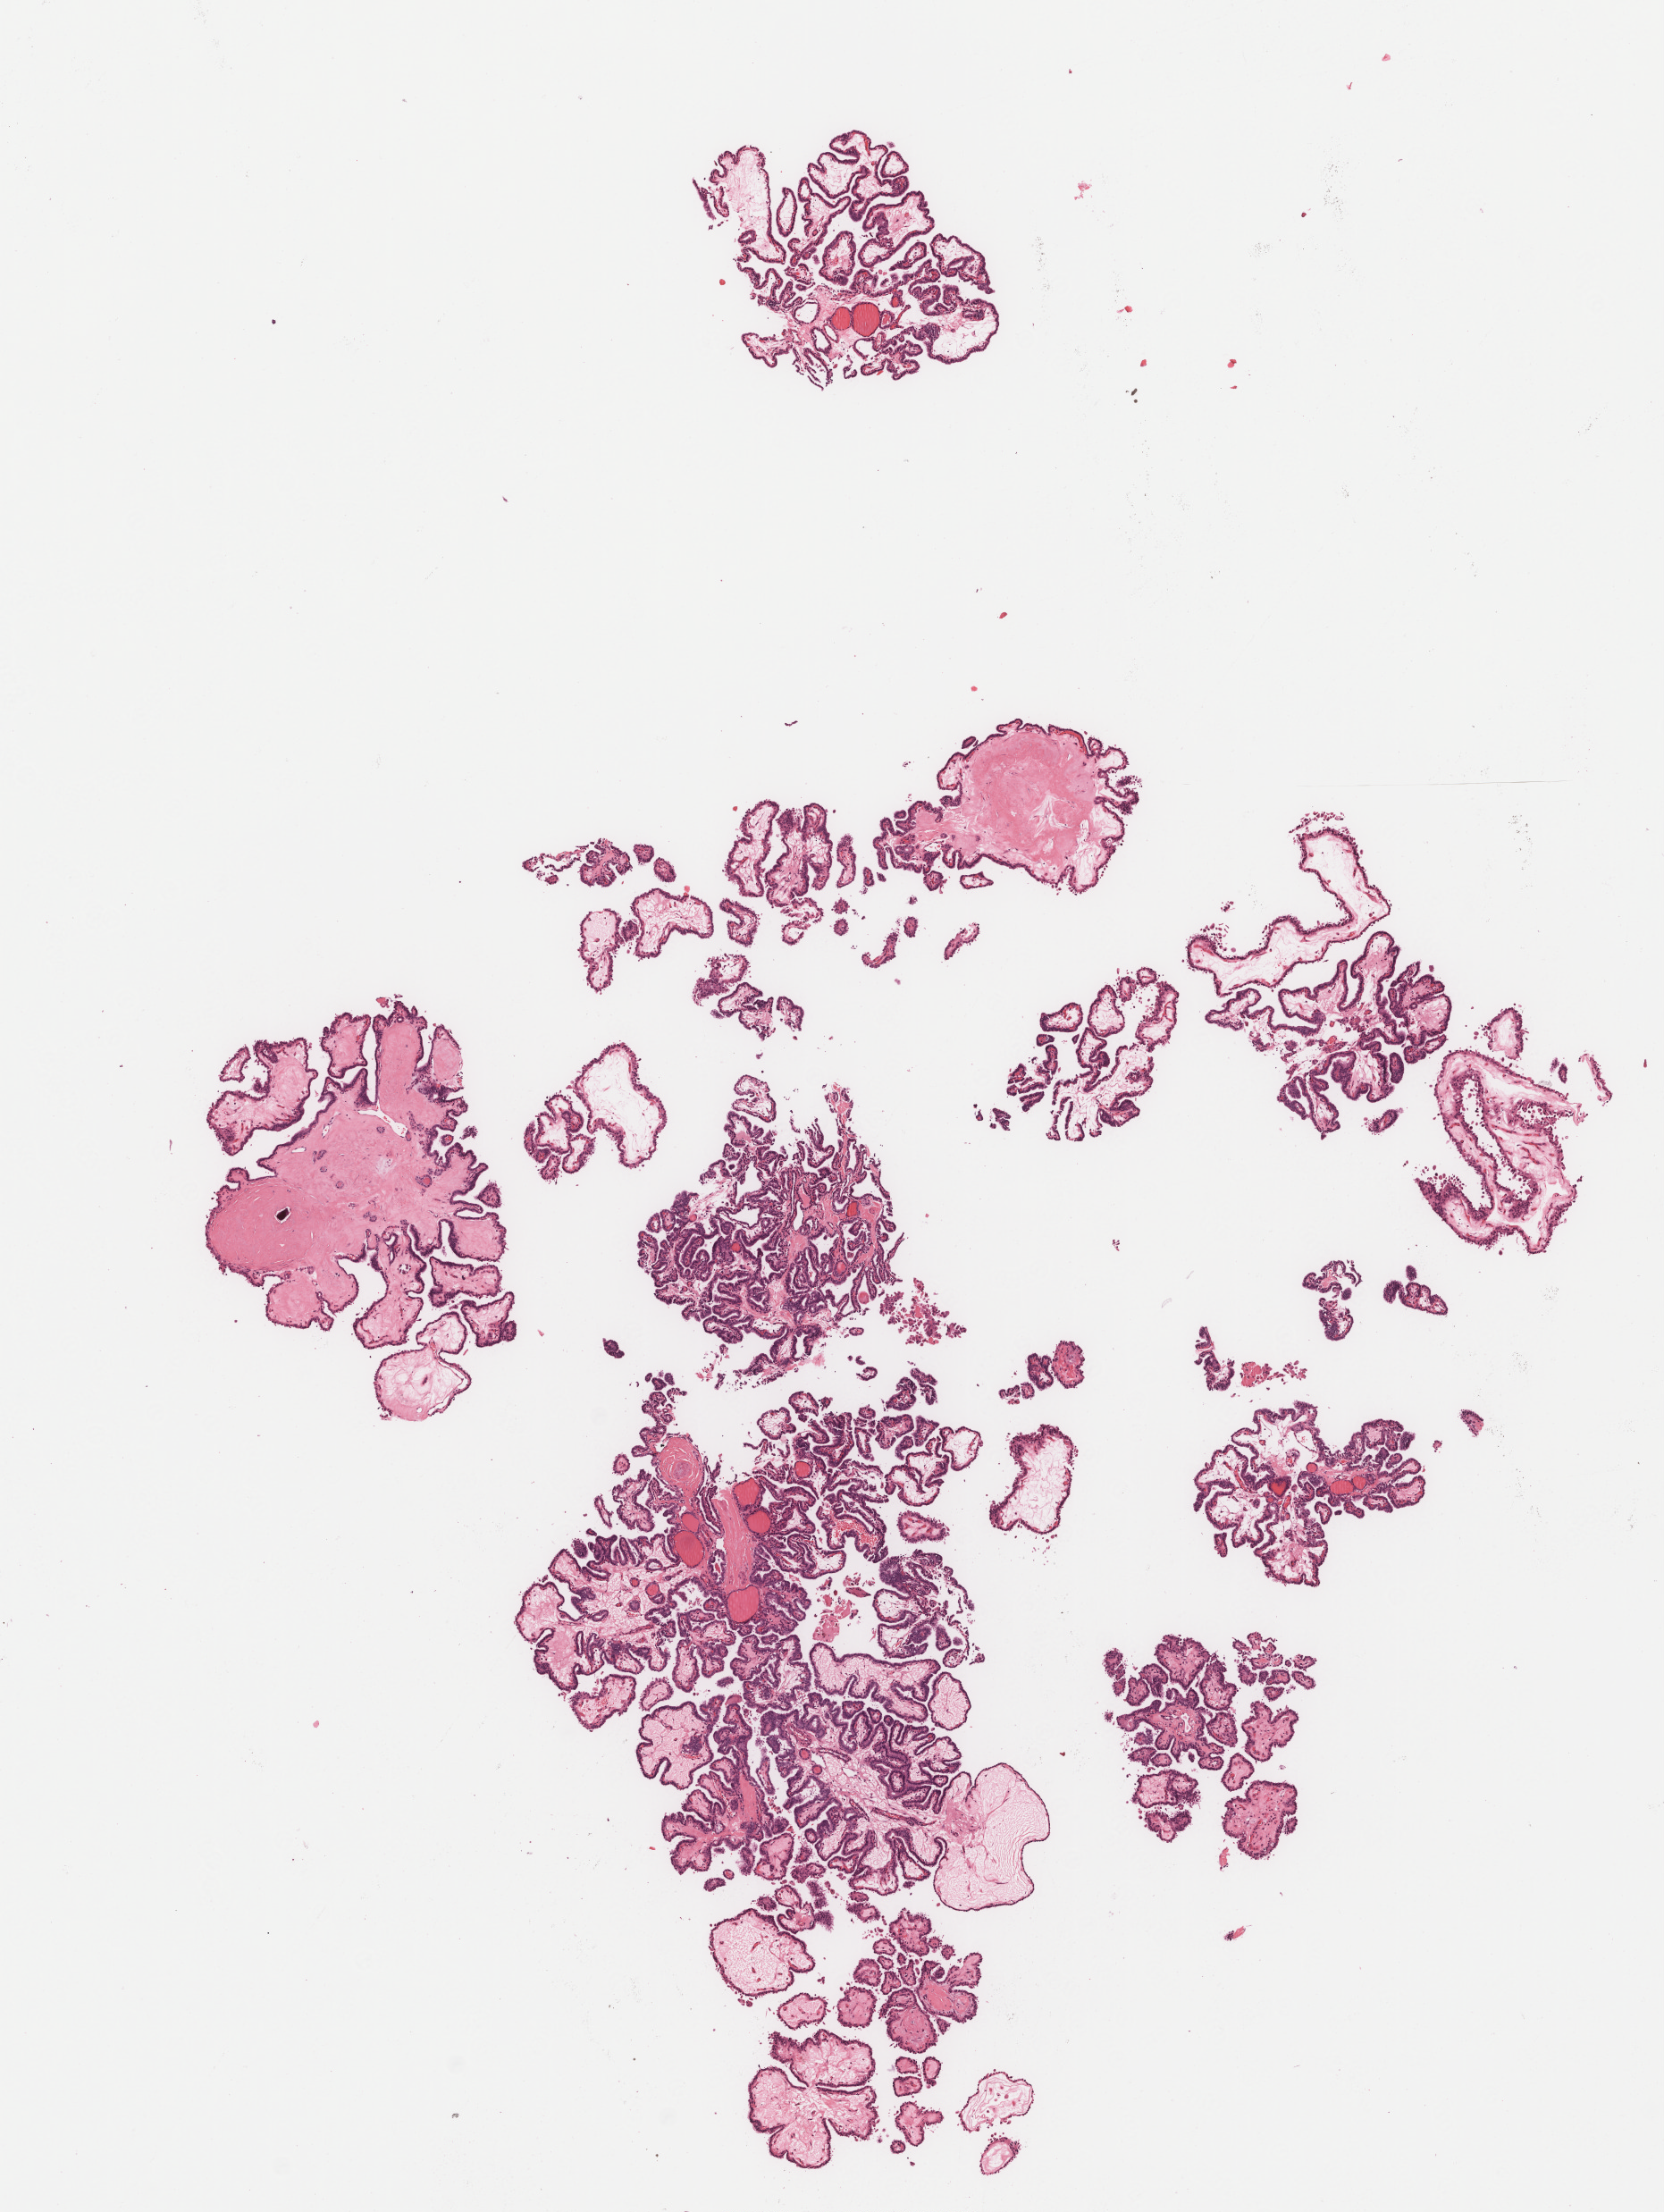
Digitized H&E-stained tissue section (whole slide), low-resolution overview of the scanned area, about 7.5 x 10.0 mm. Formalin-fixed paraffin-embedded (FFPE) diagnostic section. Primary tumour sample from the thyroid. Patient: female, age at initial diagnosis 30 years.
Laterality: midline. Diagnosis: Papillary adenocarcinoma, NOS (thyroid gland). AJCC pathologic stage: I (7th edition). Lymph nodes positive (case pathology): 17 of 25 examined.